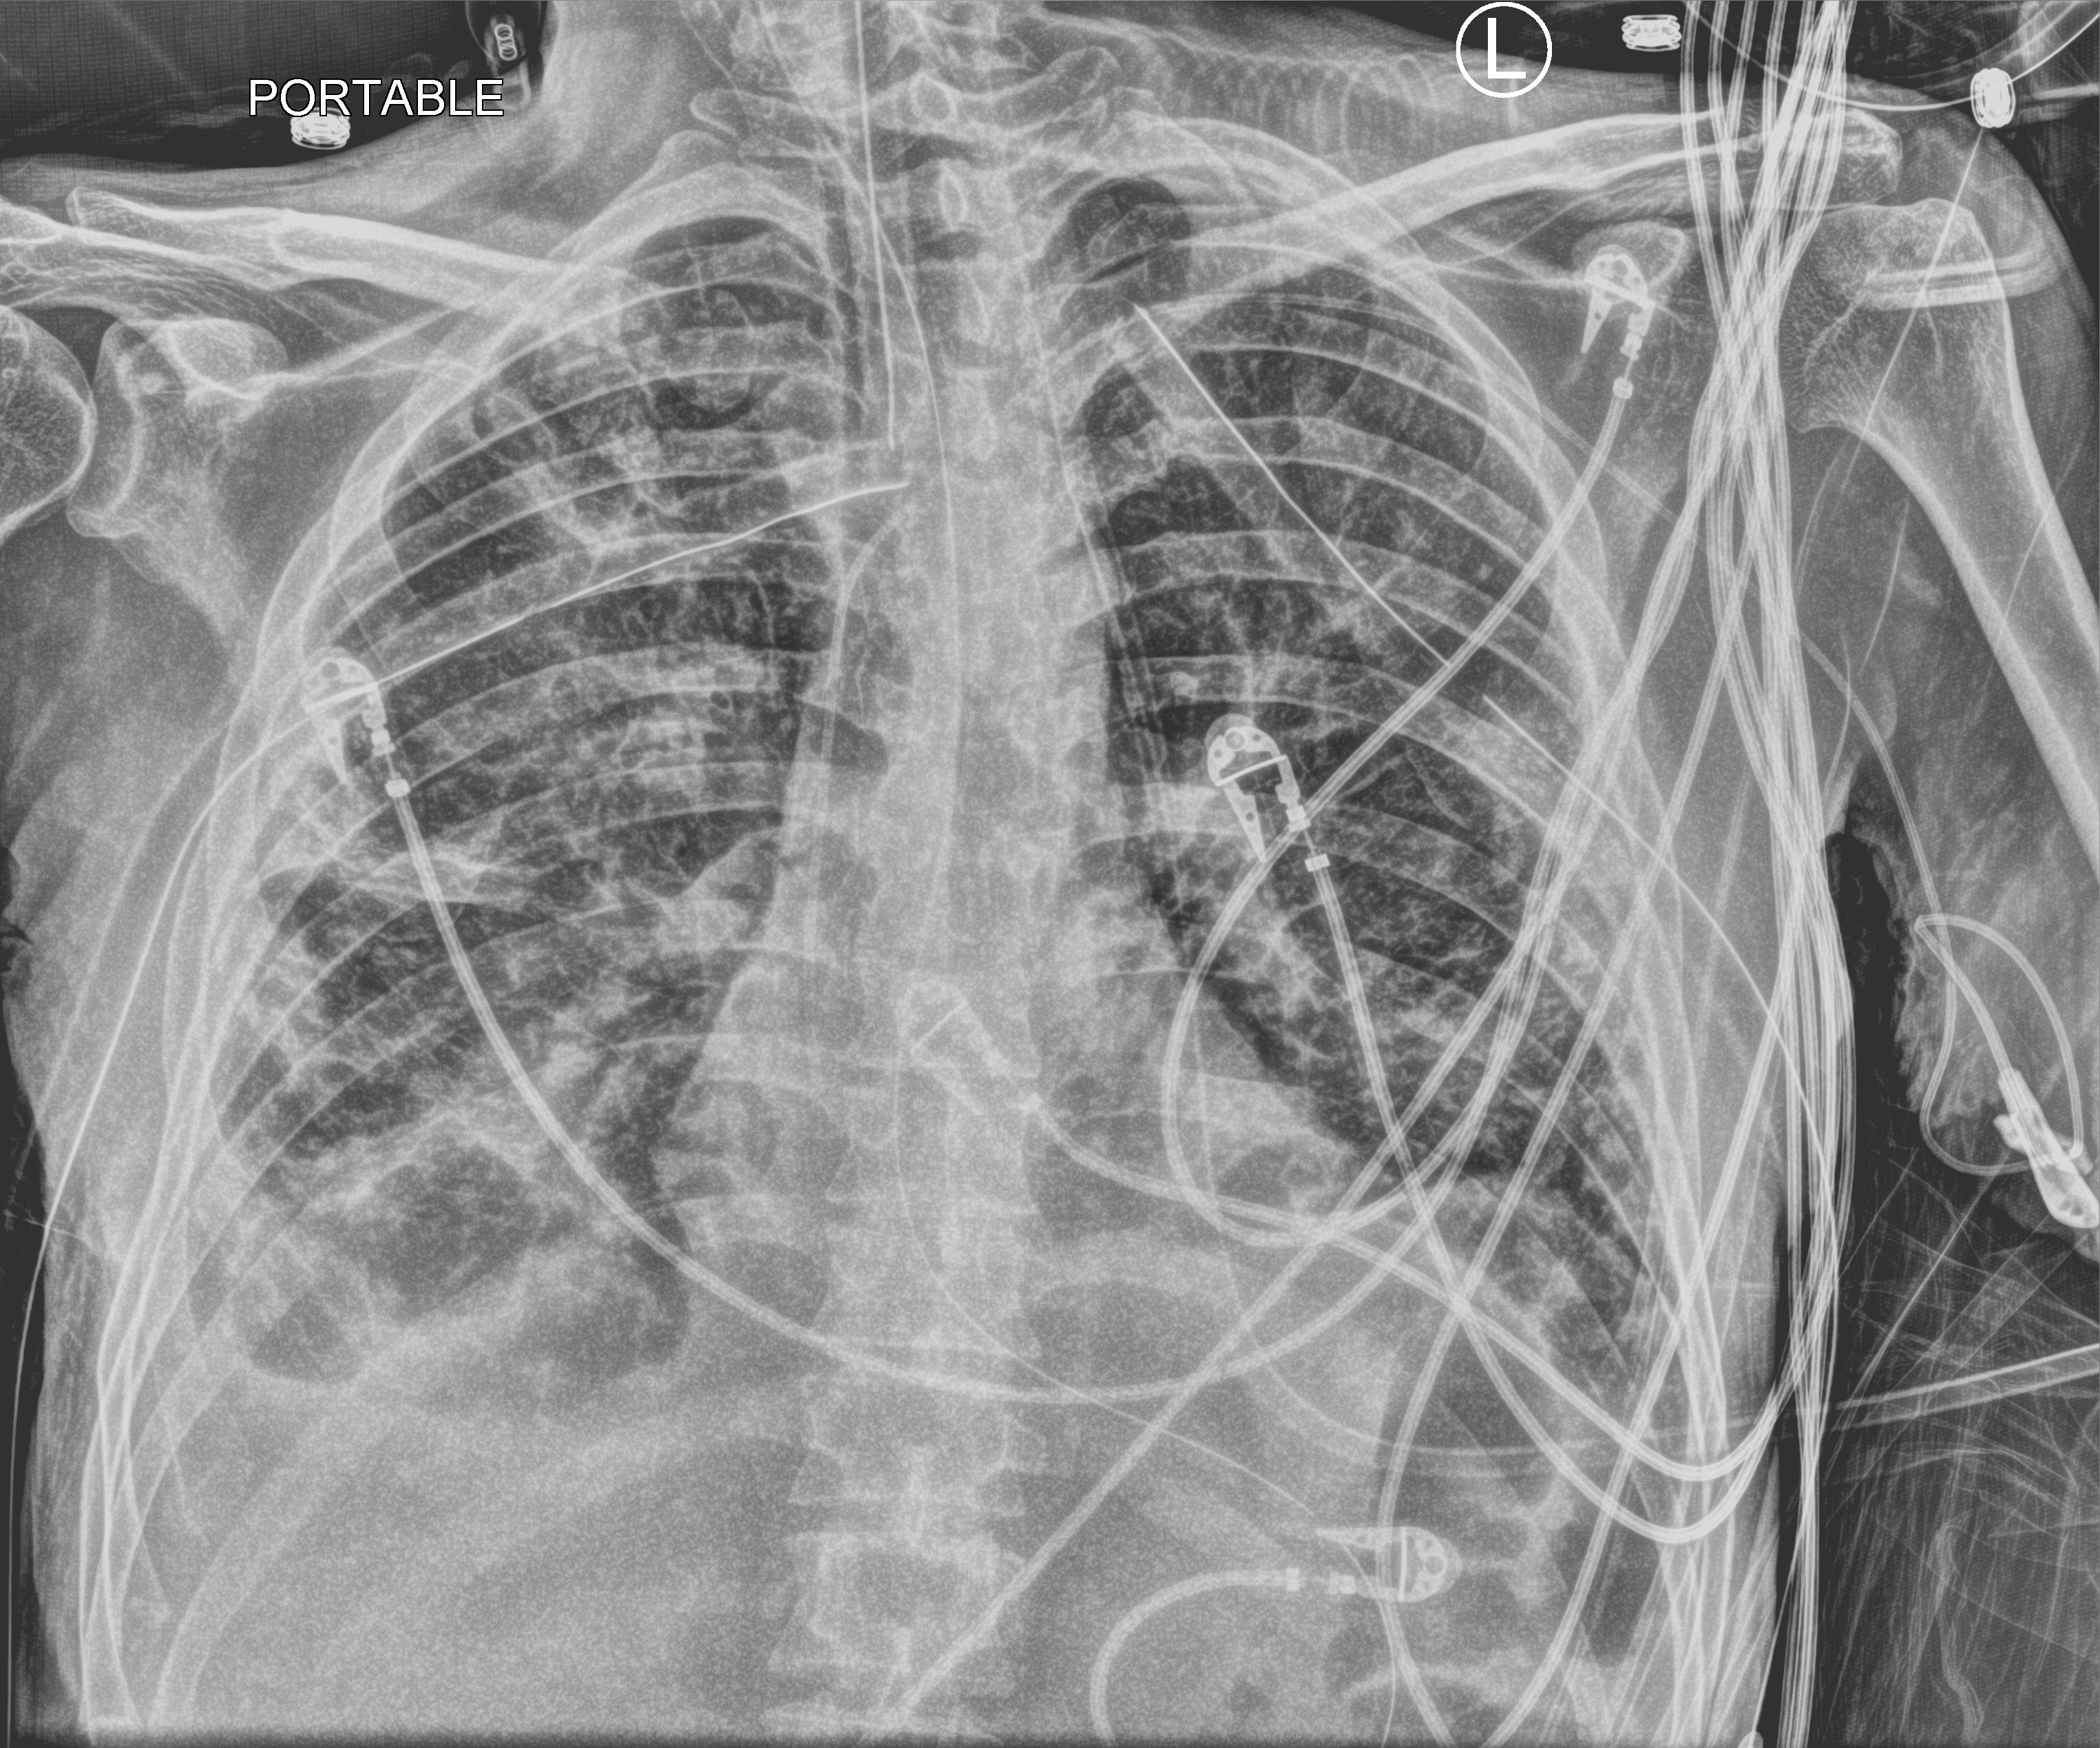
Portable chest radiograph. Patient hospitalised with COVID-19; male, aged 18–59 years.
Admission-level facts for this patient (not findings on this image; timing relative to this image not recorded): admitted to intensive care during this hospital stay: yes.